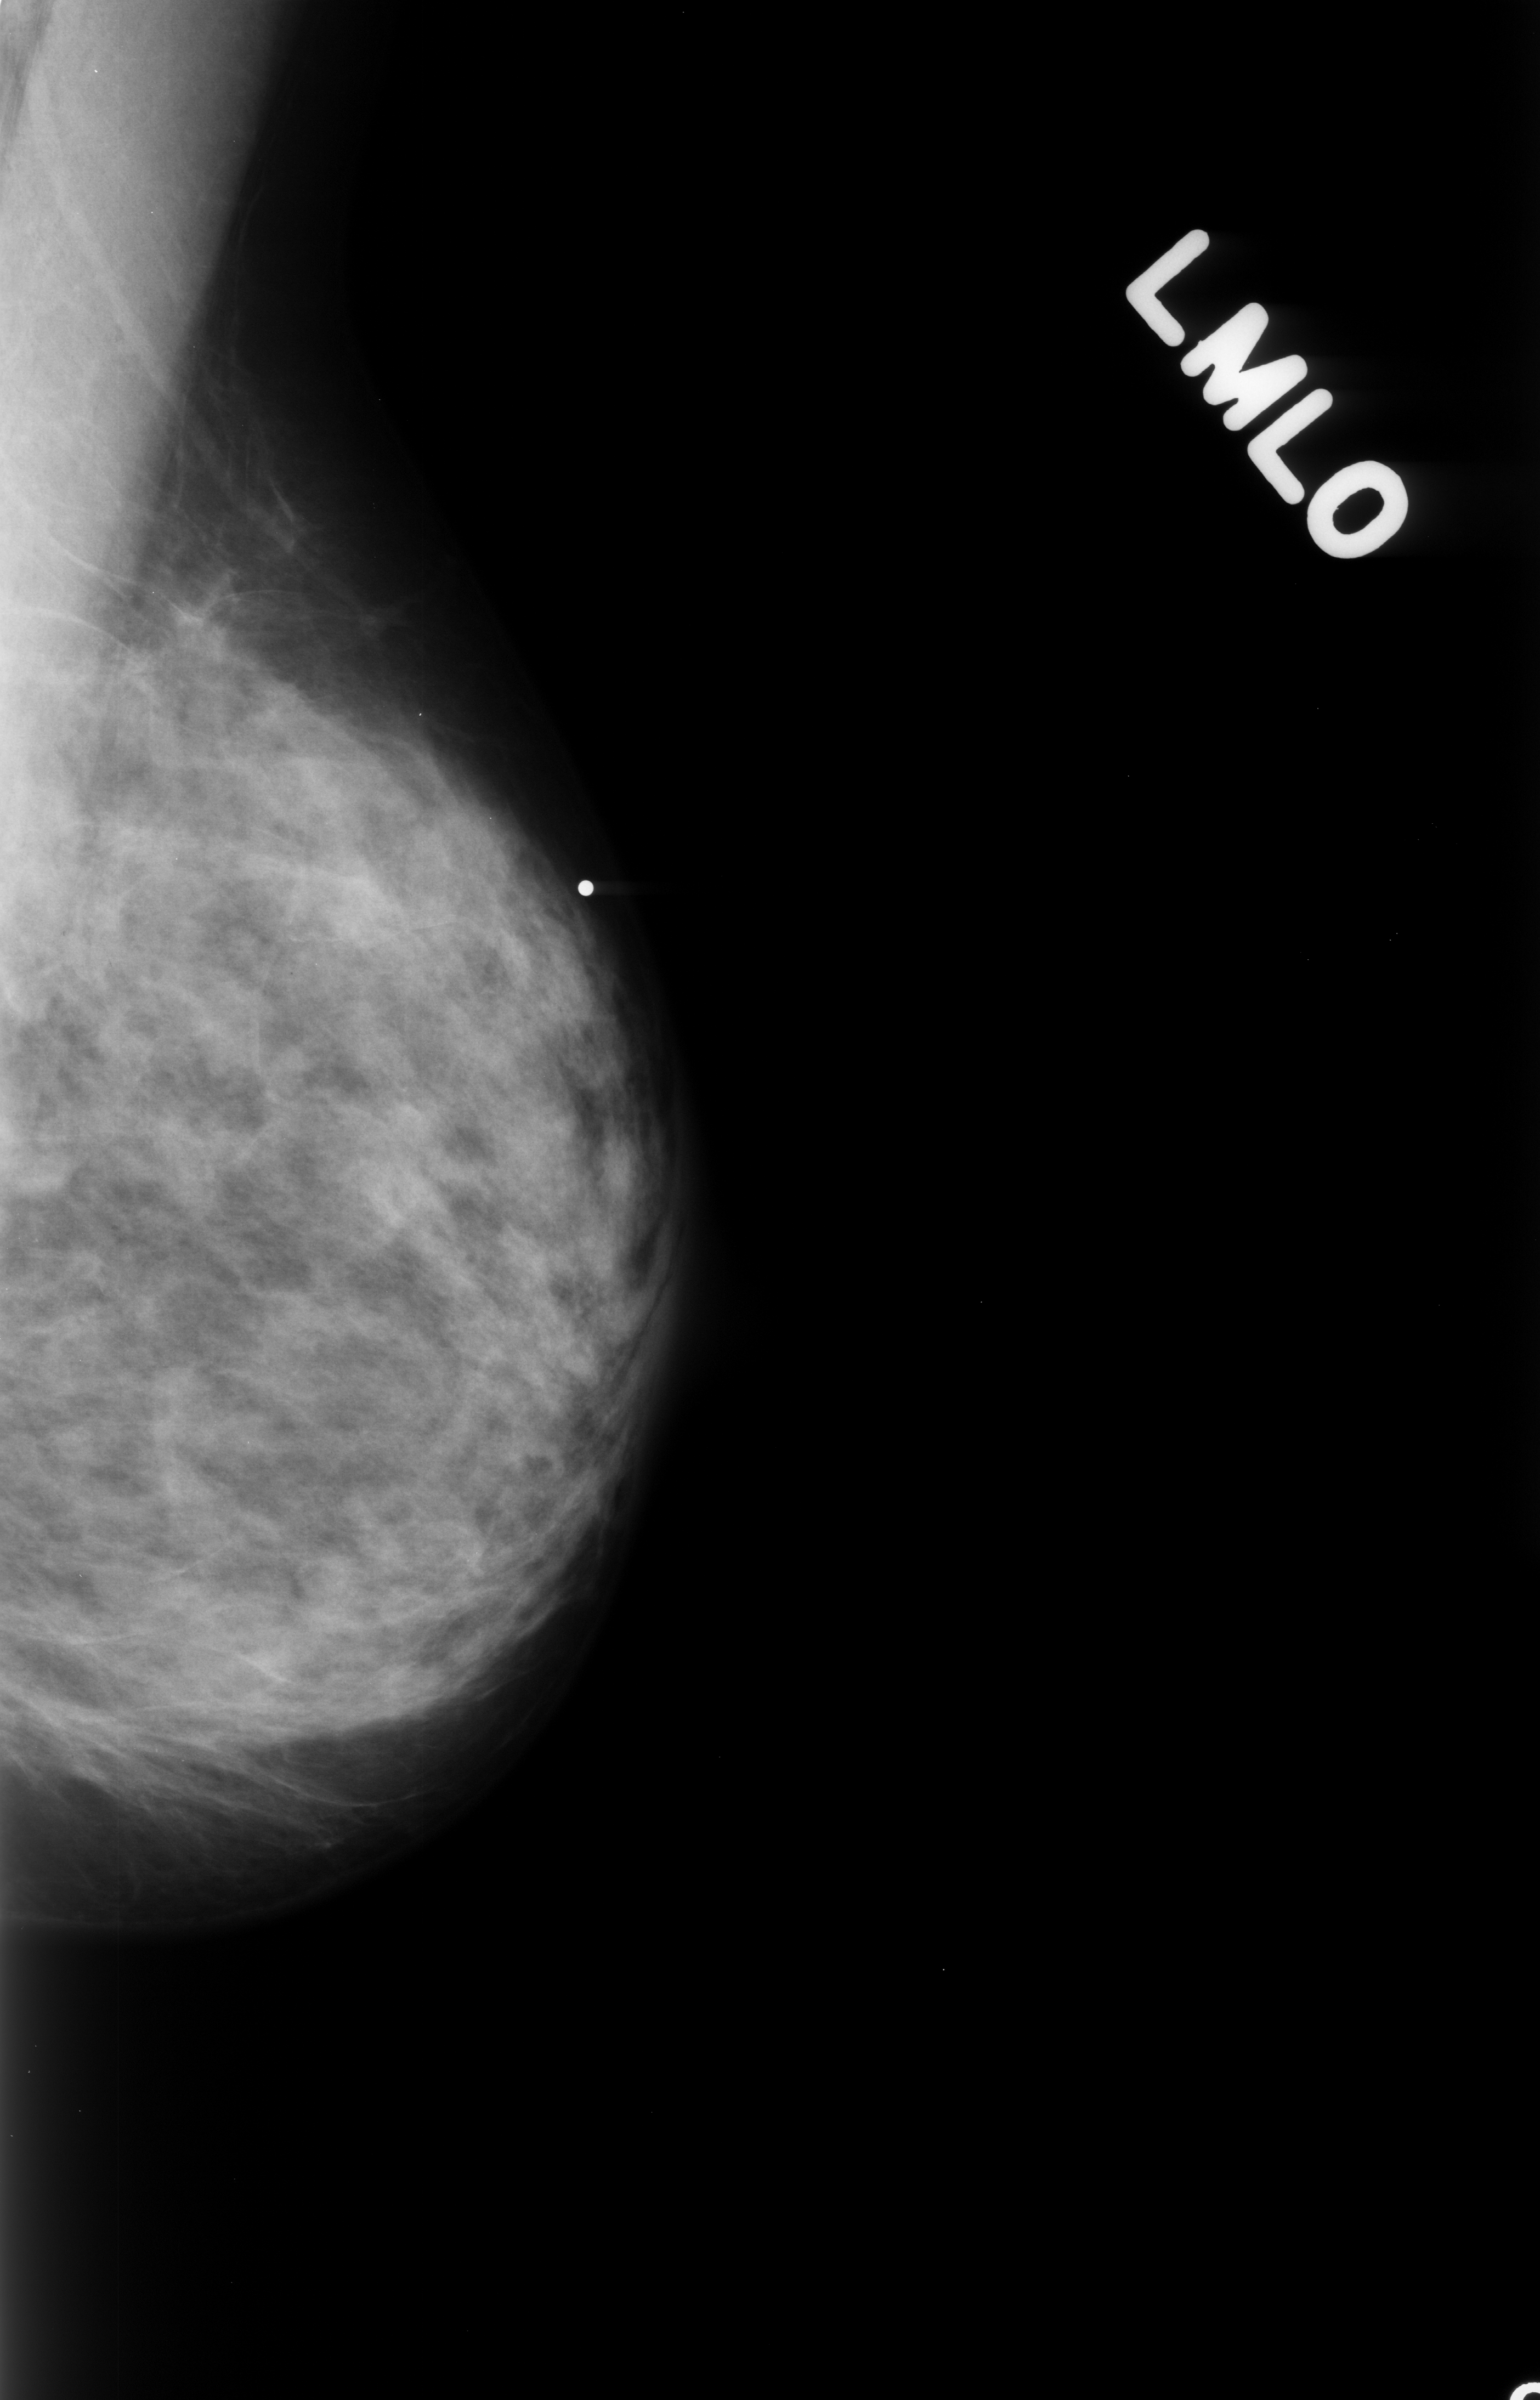
Scanned film-screen mammogram, left breast, MLO view, breast composition: heterogeneously dense (BI-RADS density category 3 of 4).
Radiologist-marked abnormalities on this image: mass, shape focal asymmetric density, margins ill defined; BI-RADS assessment category 3; subtlety rating 1 on a 1 (subtle) to 5 (obvious) scale; pathology (as recorded): benign.